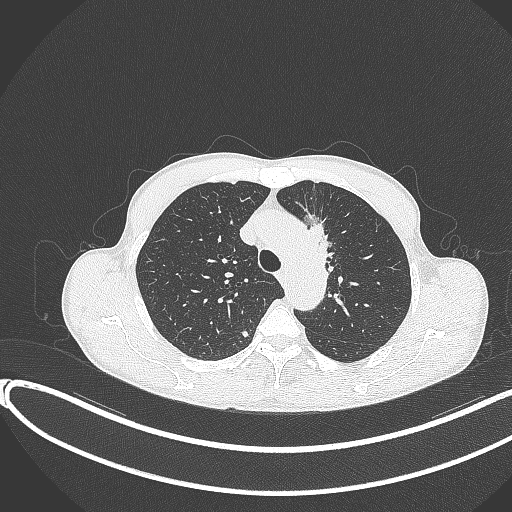
Chest CT, one axial slice; 120 kVp; lung window (W 1500 / L -600 HU); 512 × 512 image matrix, field of view 400 × 400 mm. Male patient, age 58 years. From the clinical record (not read from this slice): clinical TNM (as recorded): T1c N1 M0.
Annotated regions visible in this slice (rectangle marked by the reading radiologist):
- lung tumour (recorded histology: adenocarcinoma): box from (x=295, y=212) to (x=351, y=274) px